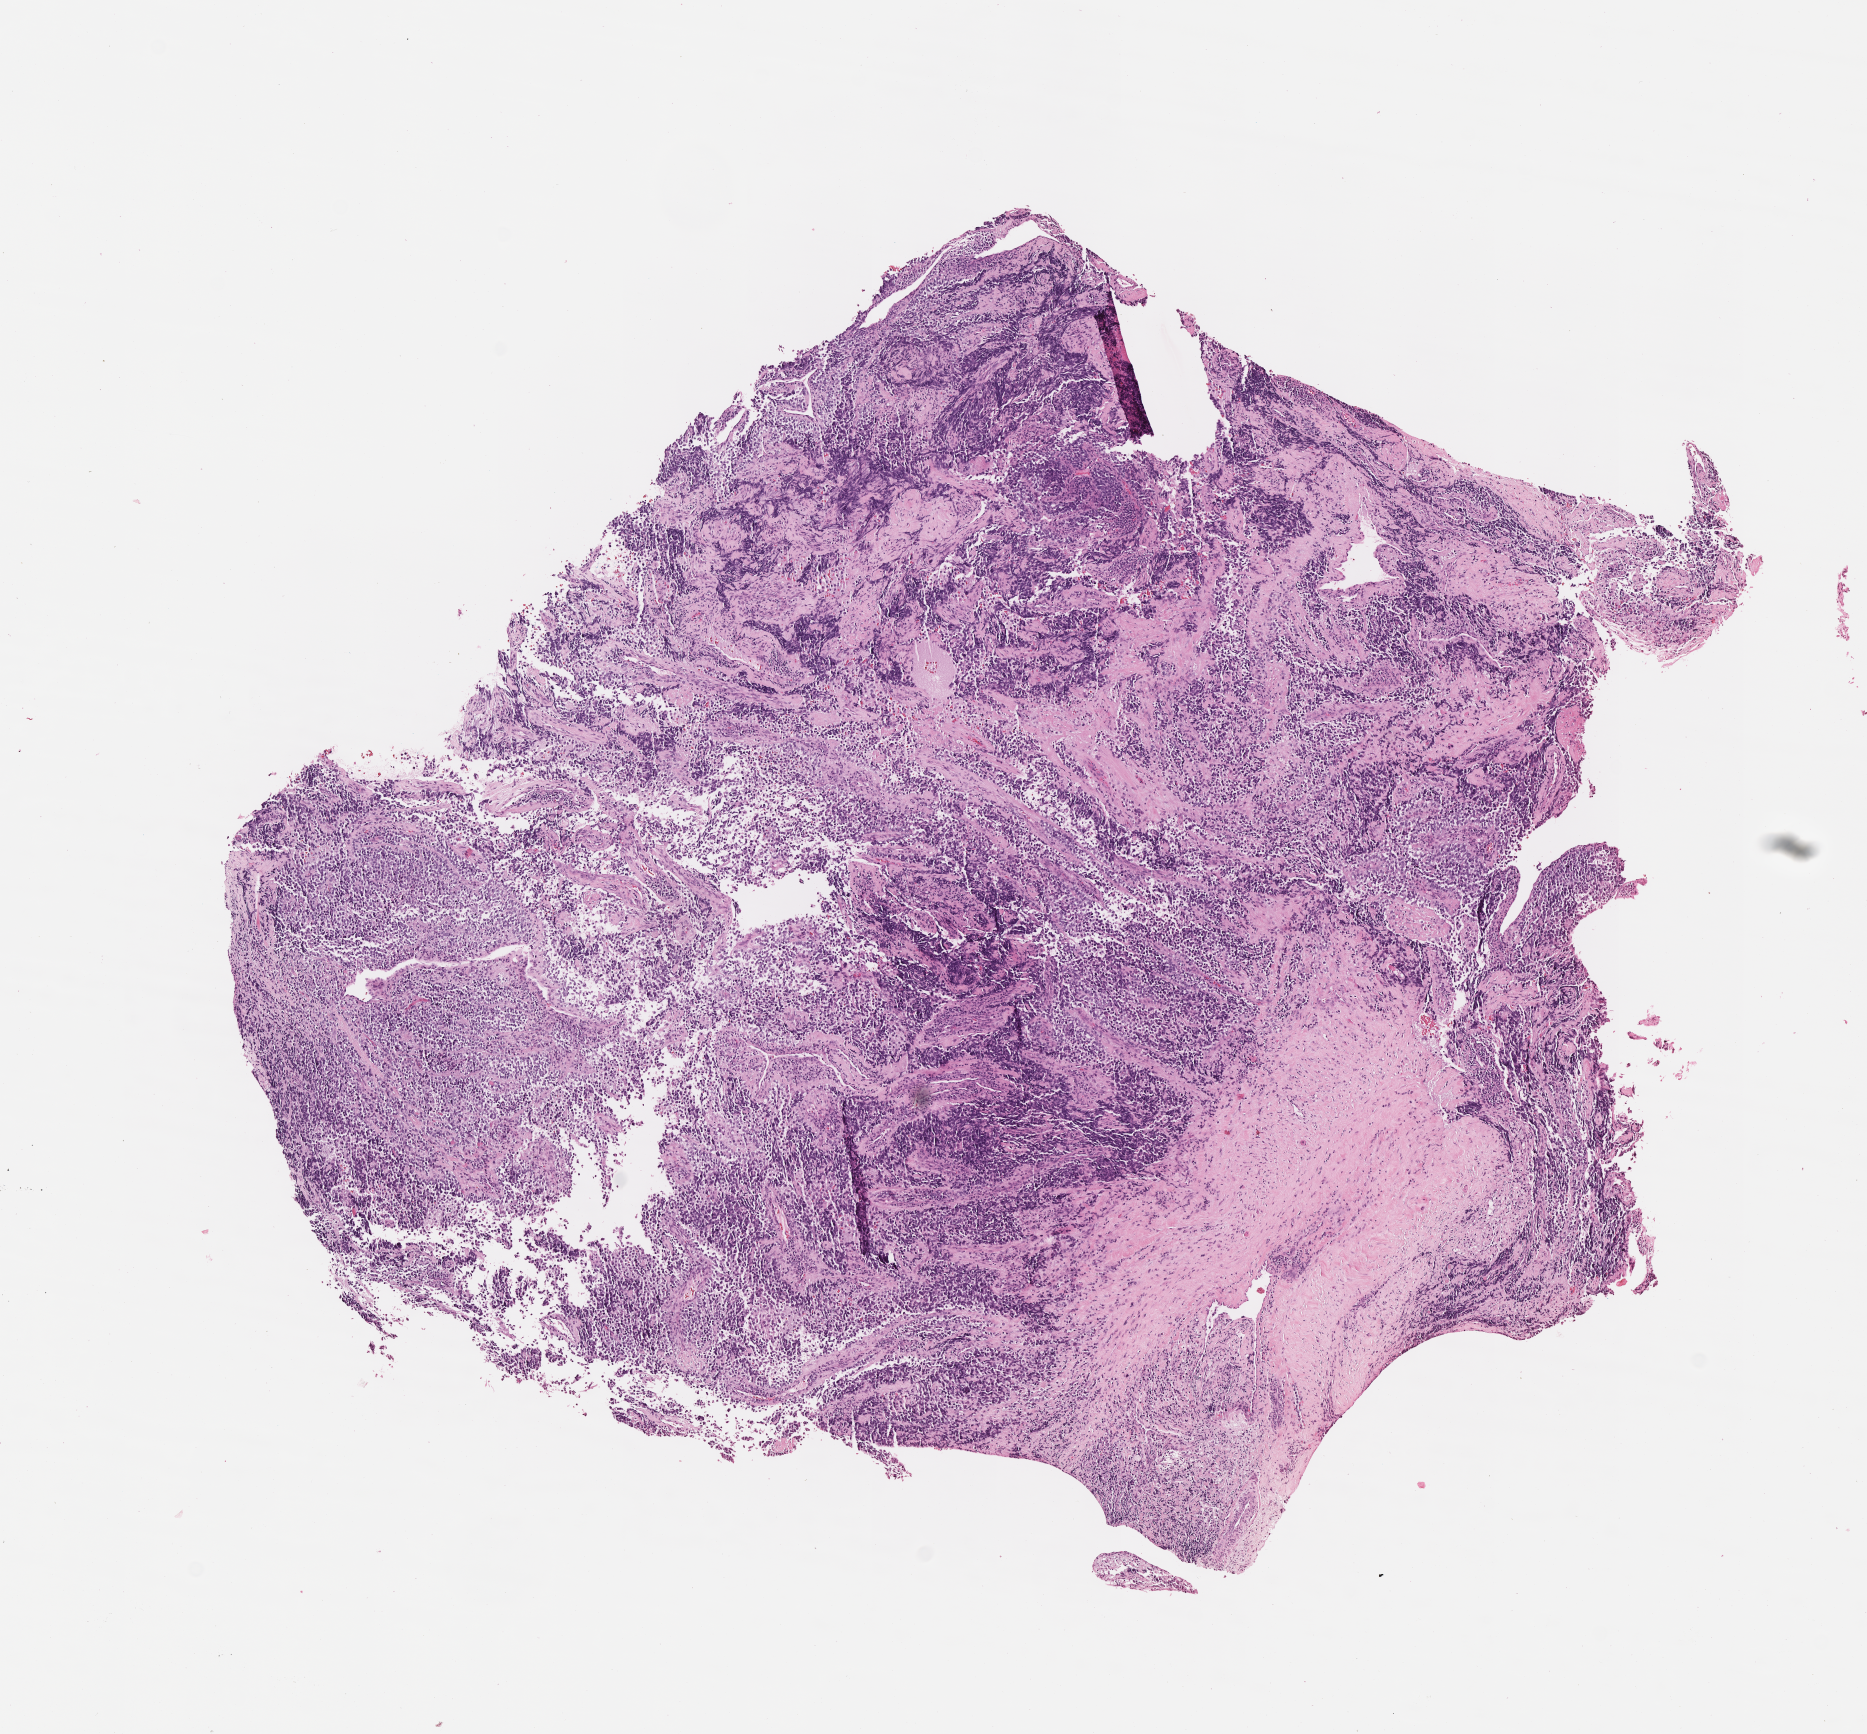
Digitized haematoxylin and eosin-stained section of tumor tissue — a low-resolution overview of the entire scanned area, about 7.5 x 7.0 mm. Formalin-fixed, paraffin-embedded (FFPE) tissue. Sample anatomic site: soft tissue, buttock-left. Female patient, age at diagnosis 4.8 years.
• diagnosis: rhabdomyosarcoma; histological classification: alveolar rhabdomyosarcoma
• metastatic status at presentation (as recorded): metastatic (confirmed)
• stage (as recorded): 4